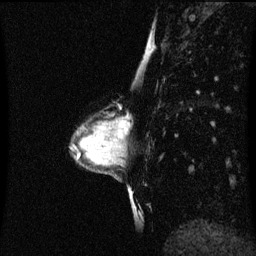
Breast MRI (dynamic contrast-enhanced), one sagittal slice. Position 27 of 60 along the scan axis. Dynamic contrast-enhanced series, image 2 of 3 at this slice position (ordered by acquisition). 1.5 T. TE 4.2 ms, TR 8.9 ms. 256 × 256 image matrix, field of view 200 × 200 mm. Patient: female, 33 years. Case-level facts recorded for this patient, not image findings: setting: breast cancer imaged before/during neoadjuvant chemotherapy; receptor status: HER2-positive.
Annotated regions visible in this slice (semi-automatically segmented with operator editing):
- analysis volume of interest (the breast-tissue region the enhancement analysis was run in; not a lesion): box from (x=107, y=114) to (x=125, y=147) px
- tumour enhancement mask (voxels above the 70 % enhancement threshold inside the analysis volume of interest): (x=118, y=120)–(x=123, y=139)